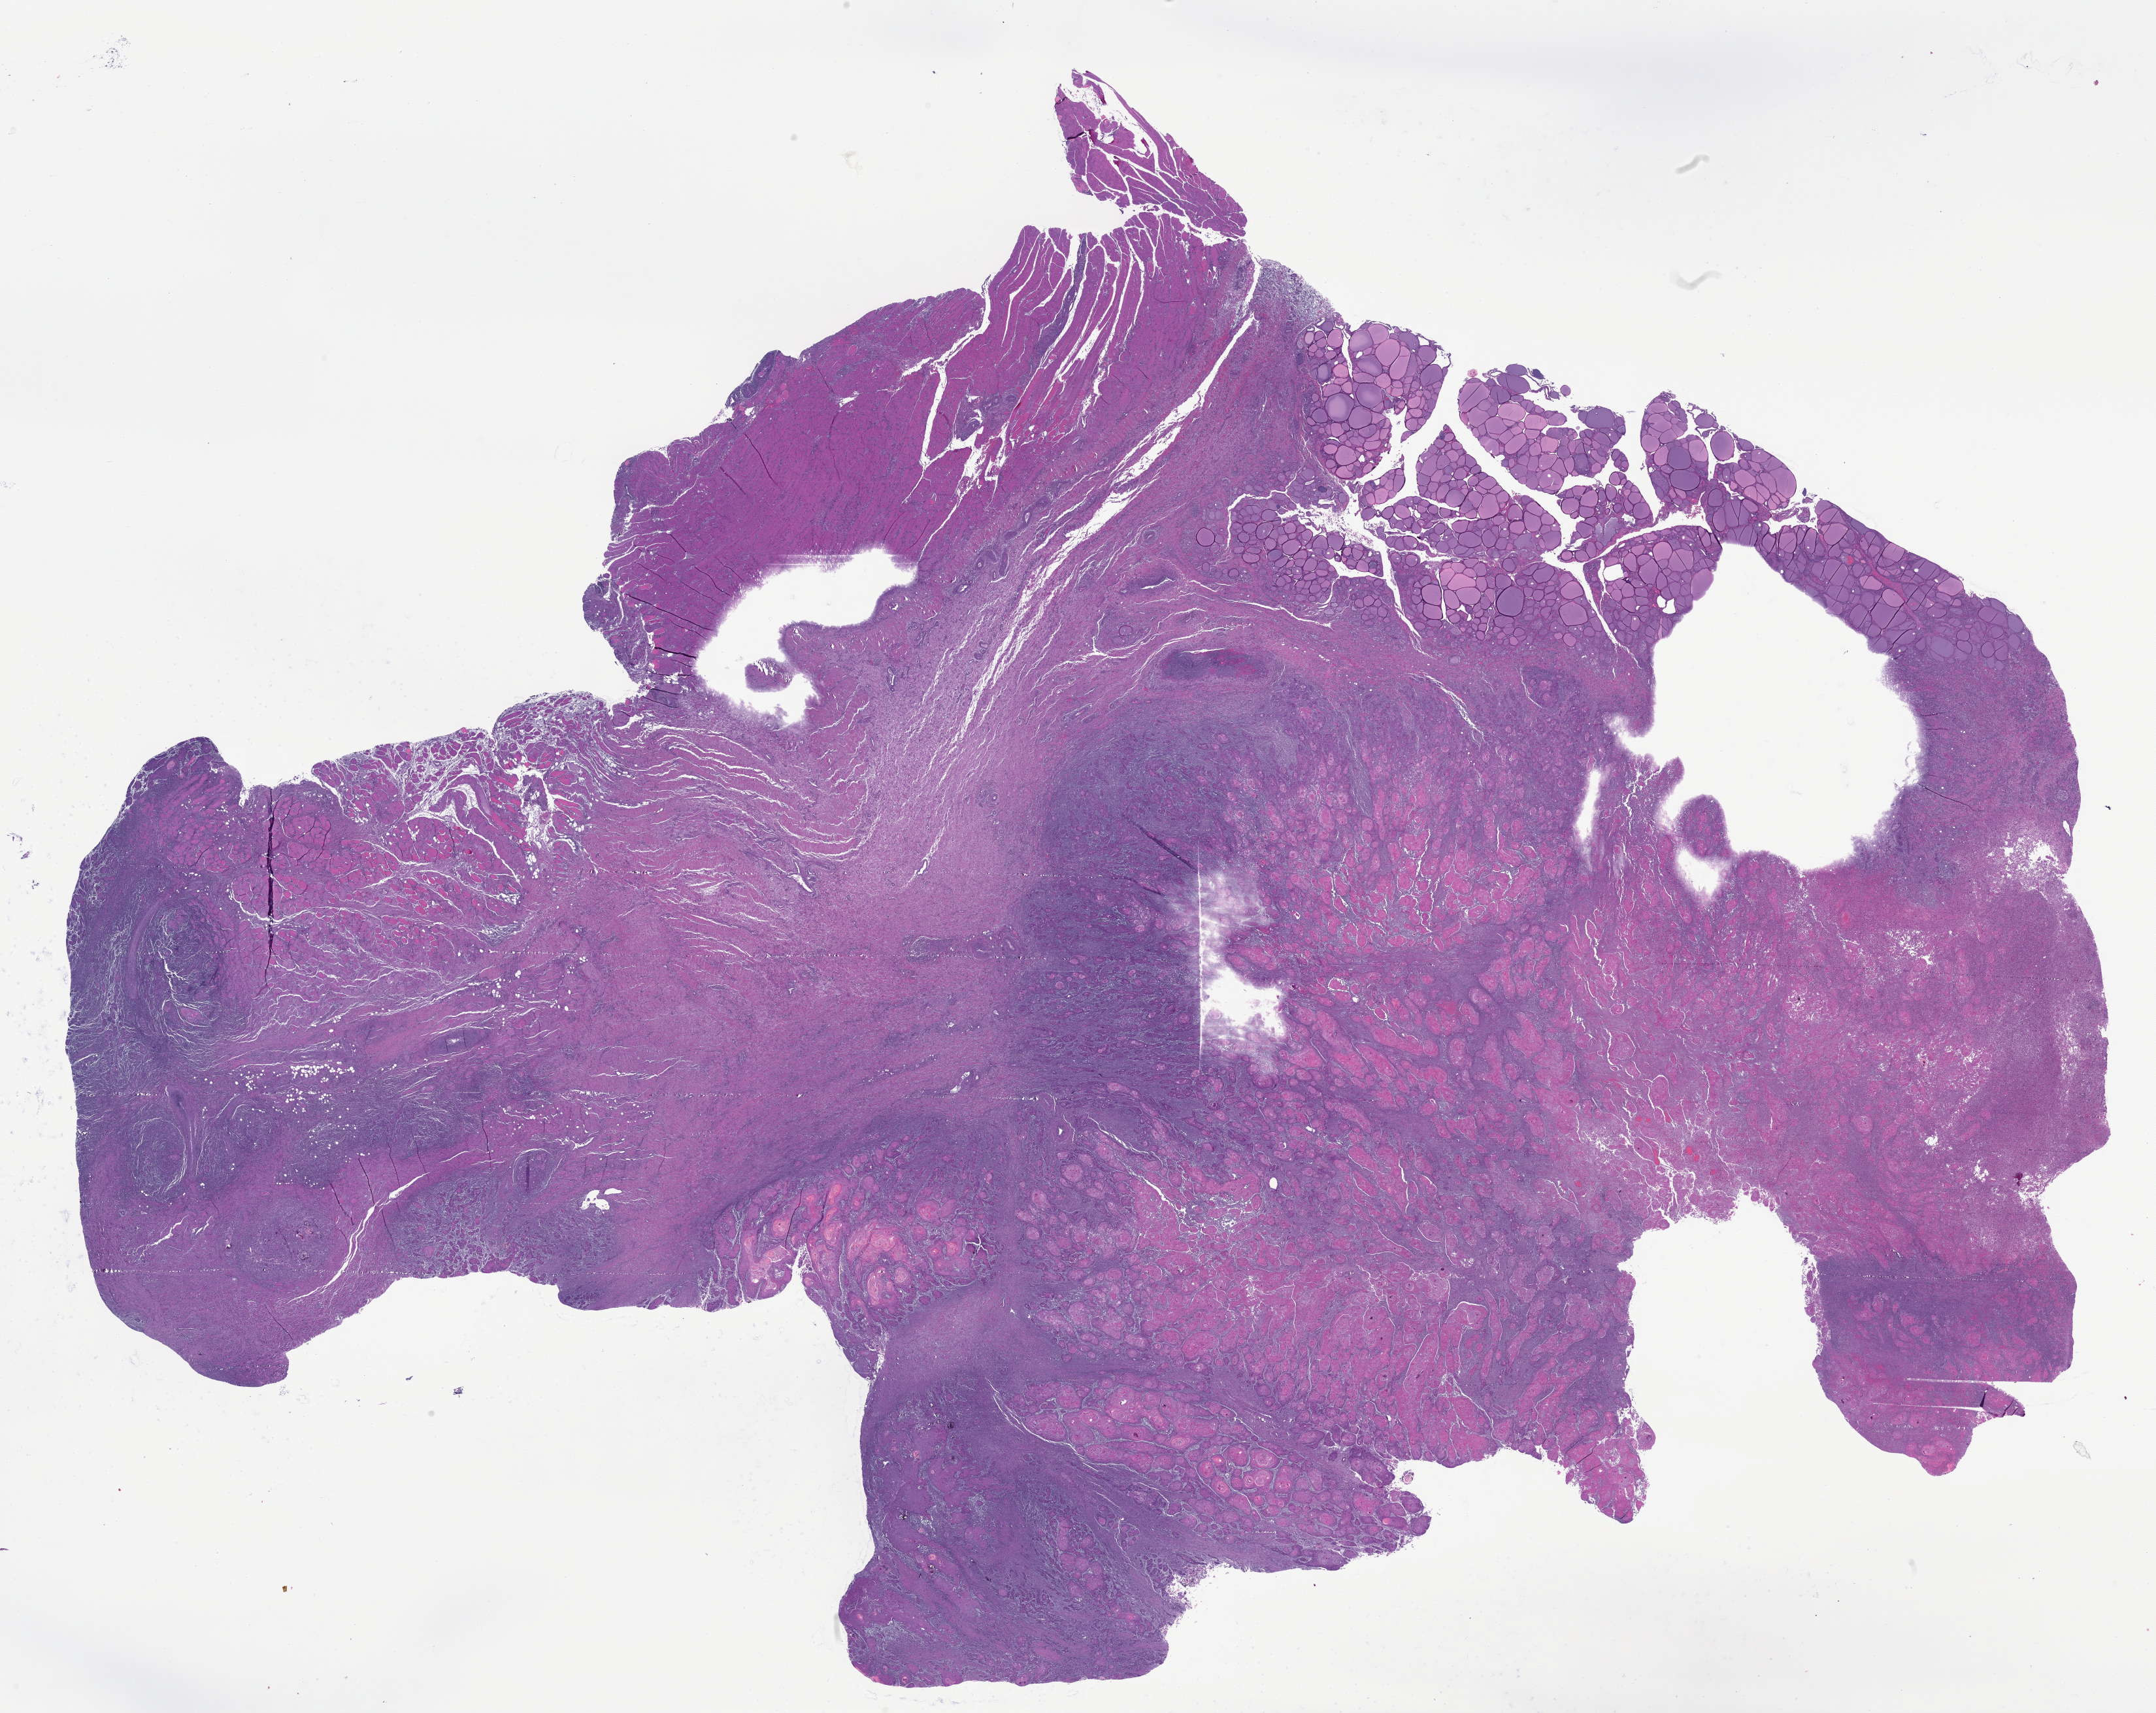
Digitized H&E tissue section (whole slide) — low-resolution overview of the scanned area, about 26.7 x 21.2 mm (from a 40x scan), formalin-fixed paraffin-embedded (FFPE) diagnostic section, head and neck, primary tumour sample. Male, age 64 years at initial diagnosis. Histologic grade: G3 (poorly differentiated).
AJCC pathologic stage: IVA (7th edition). Pathologic diagnosis: Squamous cell carcinoma, NOS (larynx, NOS).